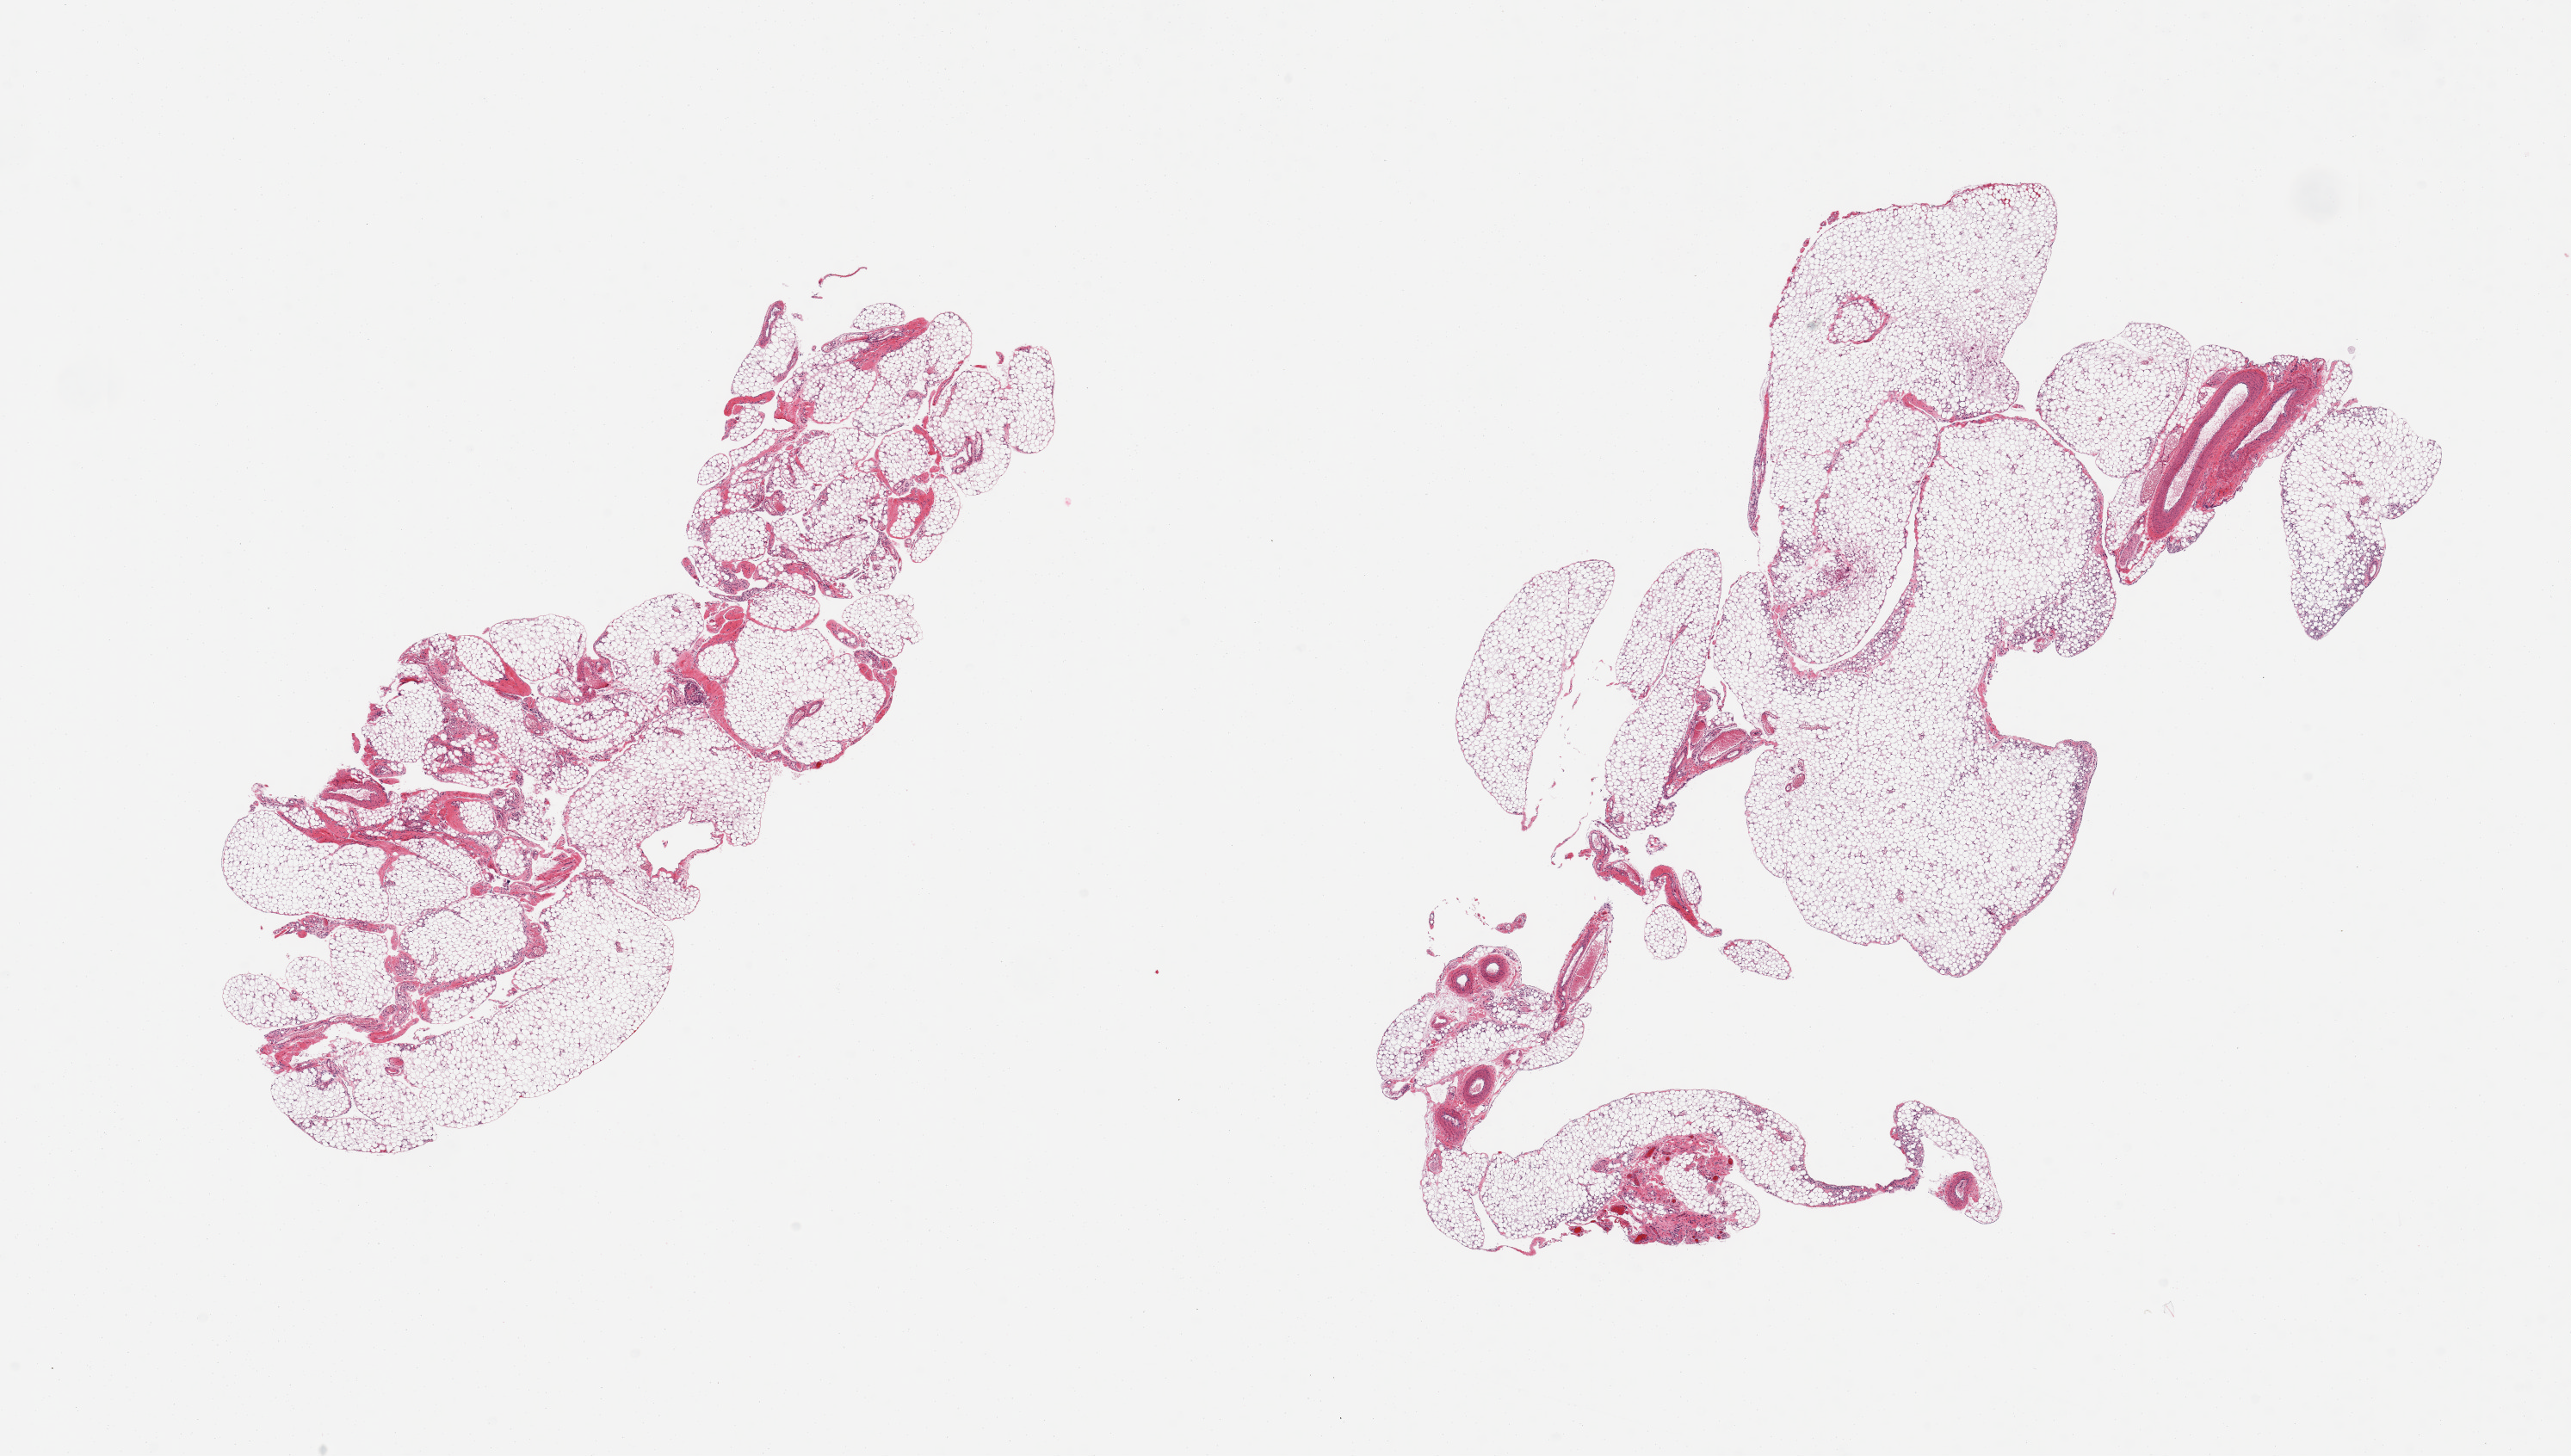
Digitized haematoxylin and eosin-stained section — low-resolution overview of the scanned area, about 23.6 x 13.4 mm. PAXgene-fixed, paraffin-embedded tissue. Section of omentum (target tissue). Donor tissue sample. Donor: male.
Reviewer comment on this tissue sample: 2 pieces ~10% fascia/vascular elements.